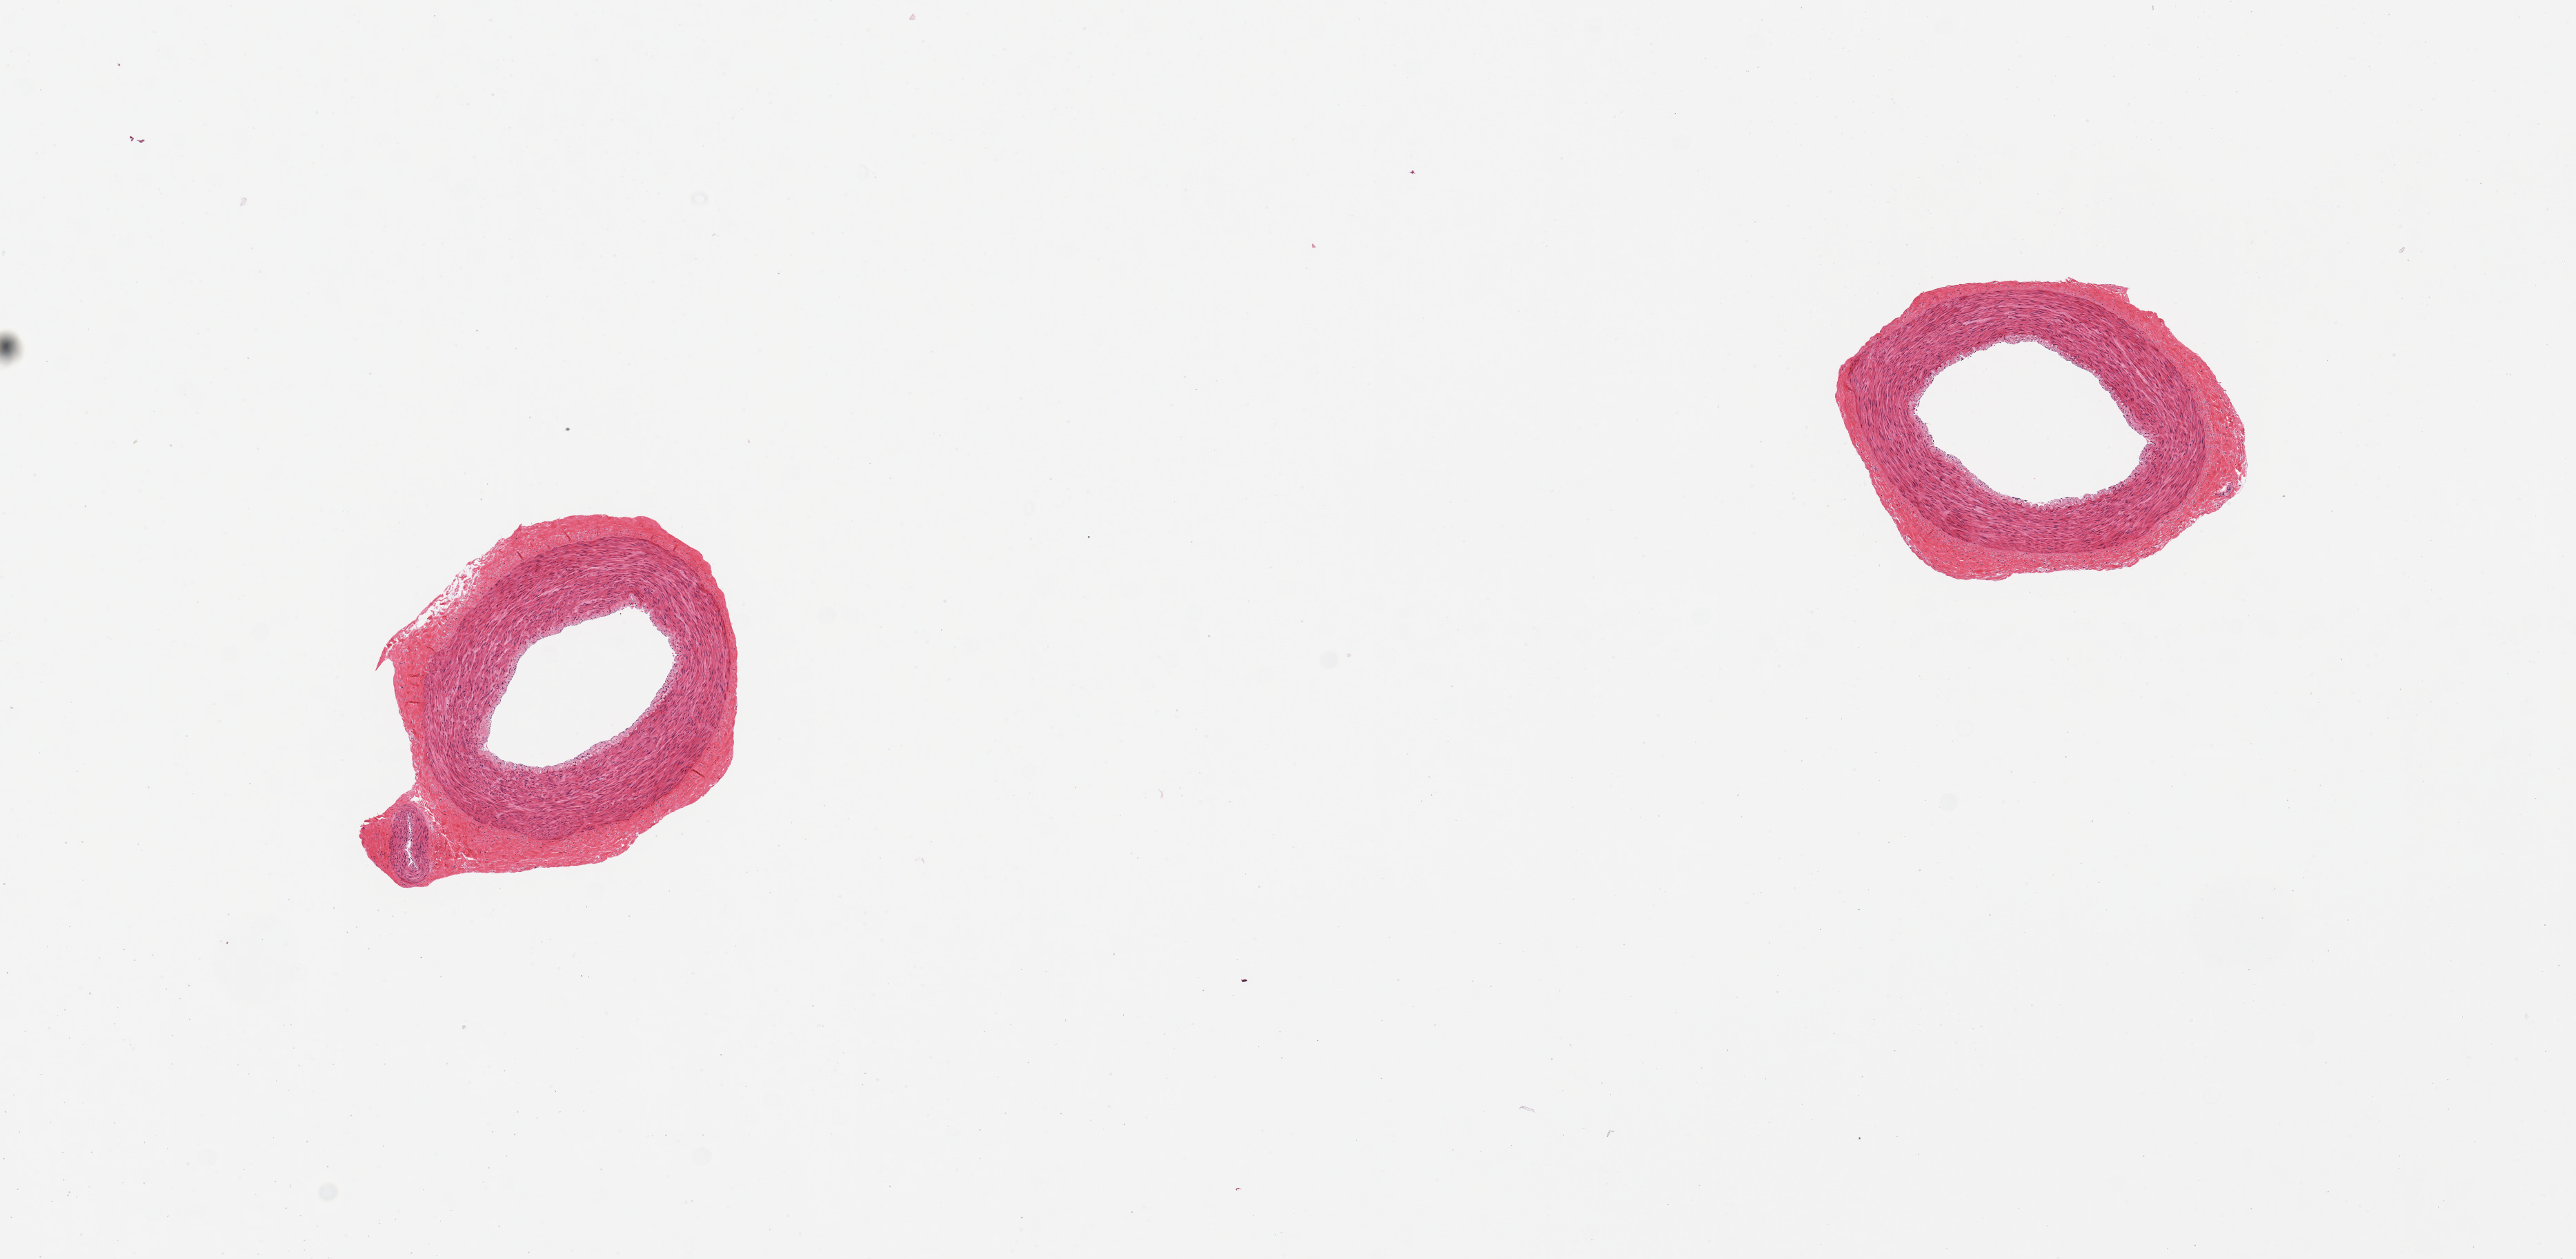
Haematoxylin and eosin whole-slide image, brightfield, whole scanned area (about 14.8 x 7.2 mm, from a 20x scan) shown as a low-resolution overview, PAXgene-fixed, paraffin-embedded tissue, sampled site (target tissue): tibial artery, tissue donor sample. Donor sex: male.
• review note (as recorded): 2 pieces; excellent normal